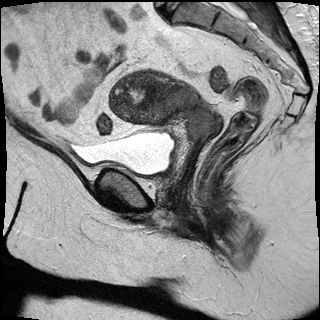
Pelvic MRI for cervical cancer, one sagittal slice. Position 16 of 30 along the scan axis. T2-weighted. 1.5 T. TE 89 ms, TR 2930 ms. 4 mm slice thickness. 320 × 320 image matrix, field of view 260 × 260 mm. Female patient, age 53 years.
Outlined on this slice (manually delineated by an expert):
- uterus and cervix: bounding box (x1, y1, x2, y2) in pixels: (110, 70, 222, 142)